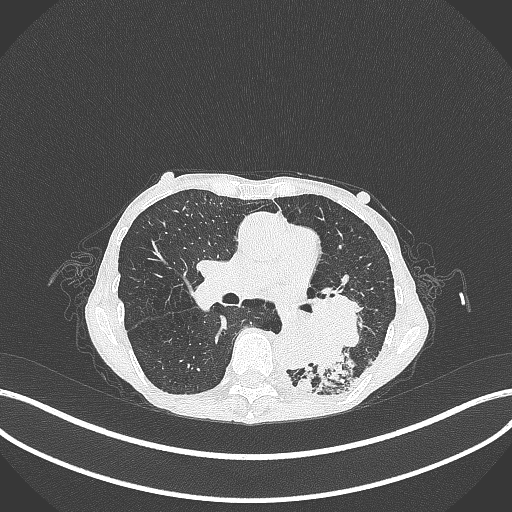
Chest CT, one axial slice; position 145 of 347 along the scan axis; 120 kVp; lung window (W 1500 / L -600 HU); 512 × 512 image matrix, field of view 400 × 400 mm. Female patient, age 70 years. From the clinical record (not read from this slice): clinical TNM (as recorded): T3 N0 M0; histopathological grade: G3.
Outlined on this slice (rectangle marked by the reading radiologist):
- lung tumour (recorded histology: small cell carcinoma): bounding box (x1, y1, x2, y2) in pixels: (294, 282, 369, 386)